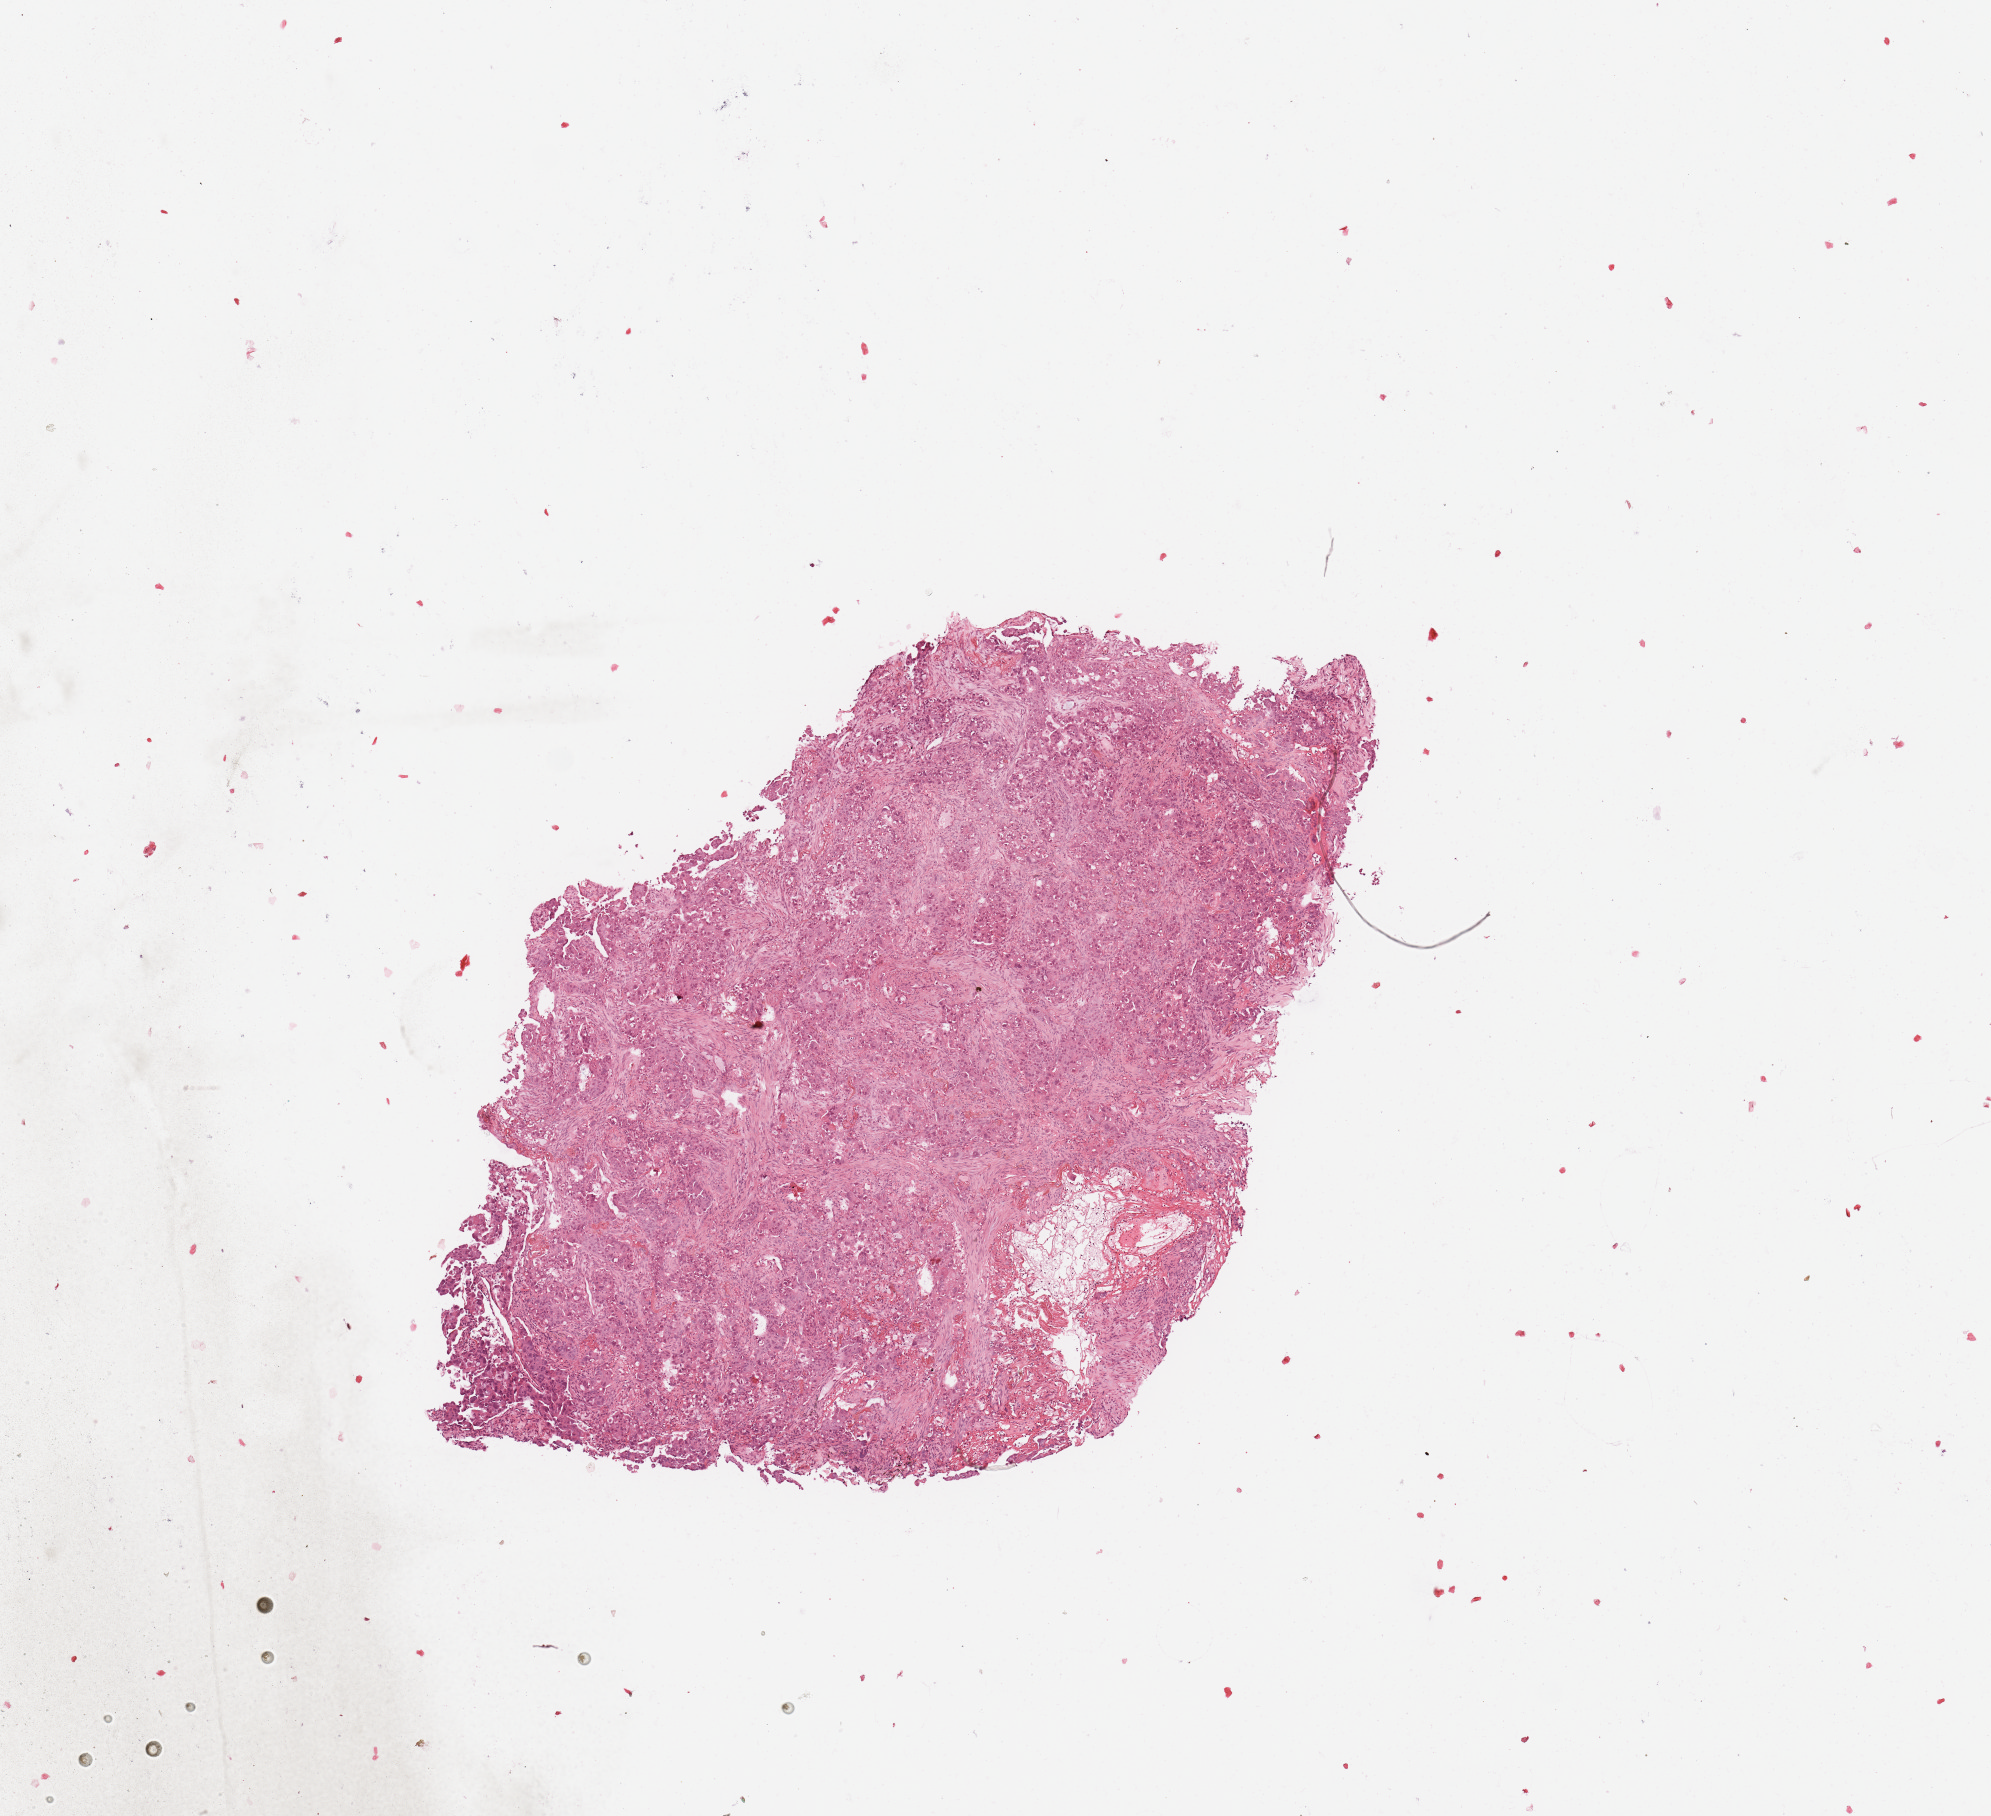
H&E whole-slide image, shown as a low-resolution overview of the whole scanned area (about 7.9 x 7.2 mm, slide scanned at 20x); tumour tissue sample, lung. Male, 51 y/o. Histologic grade: G2 (moderately differentiated).
AJCC pathologic stage: IB. Primary tumour site (as recorded): left upper lobe. Histologic diagnosis: Adenocarcinoma, NOS.